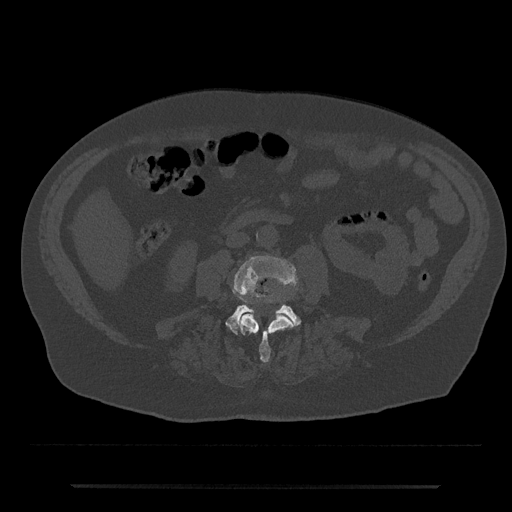
CT including the spine, one axial slice. Position 383 of 797 along the scan axis. 120 kVp. Bone window (W 1800 / L 400 HU). 0.5 mm slice thickness. 512 × 512 image matrix, field of view 434 × 434 mm. Patient: male, 80 years. From the clinical record (not read from this slice): primary cancer: prostate.
Outlined on this slice (semi-automatically segmented with operator editing):
- L3 vertebra: bounding box [x1, y1, x2, y2] px = [233, 255, 297, 363]
- L4 vertebra: [226, 297, 301, 335]